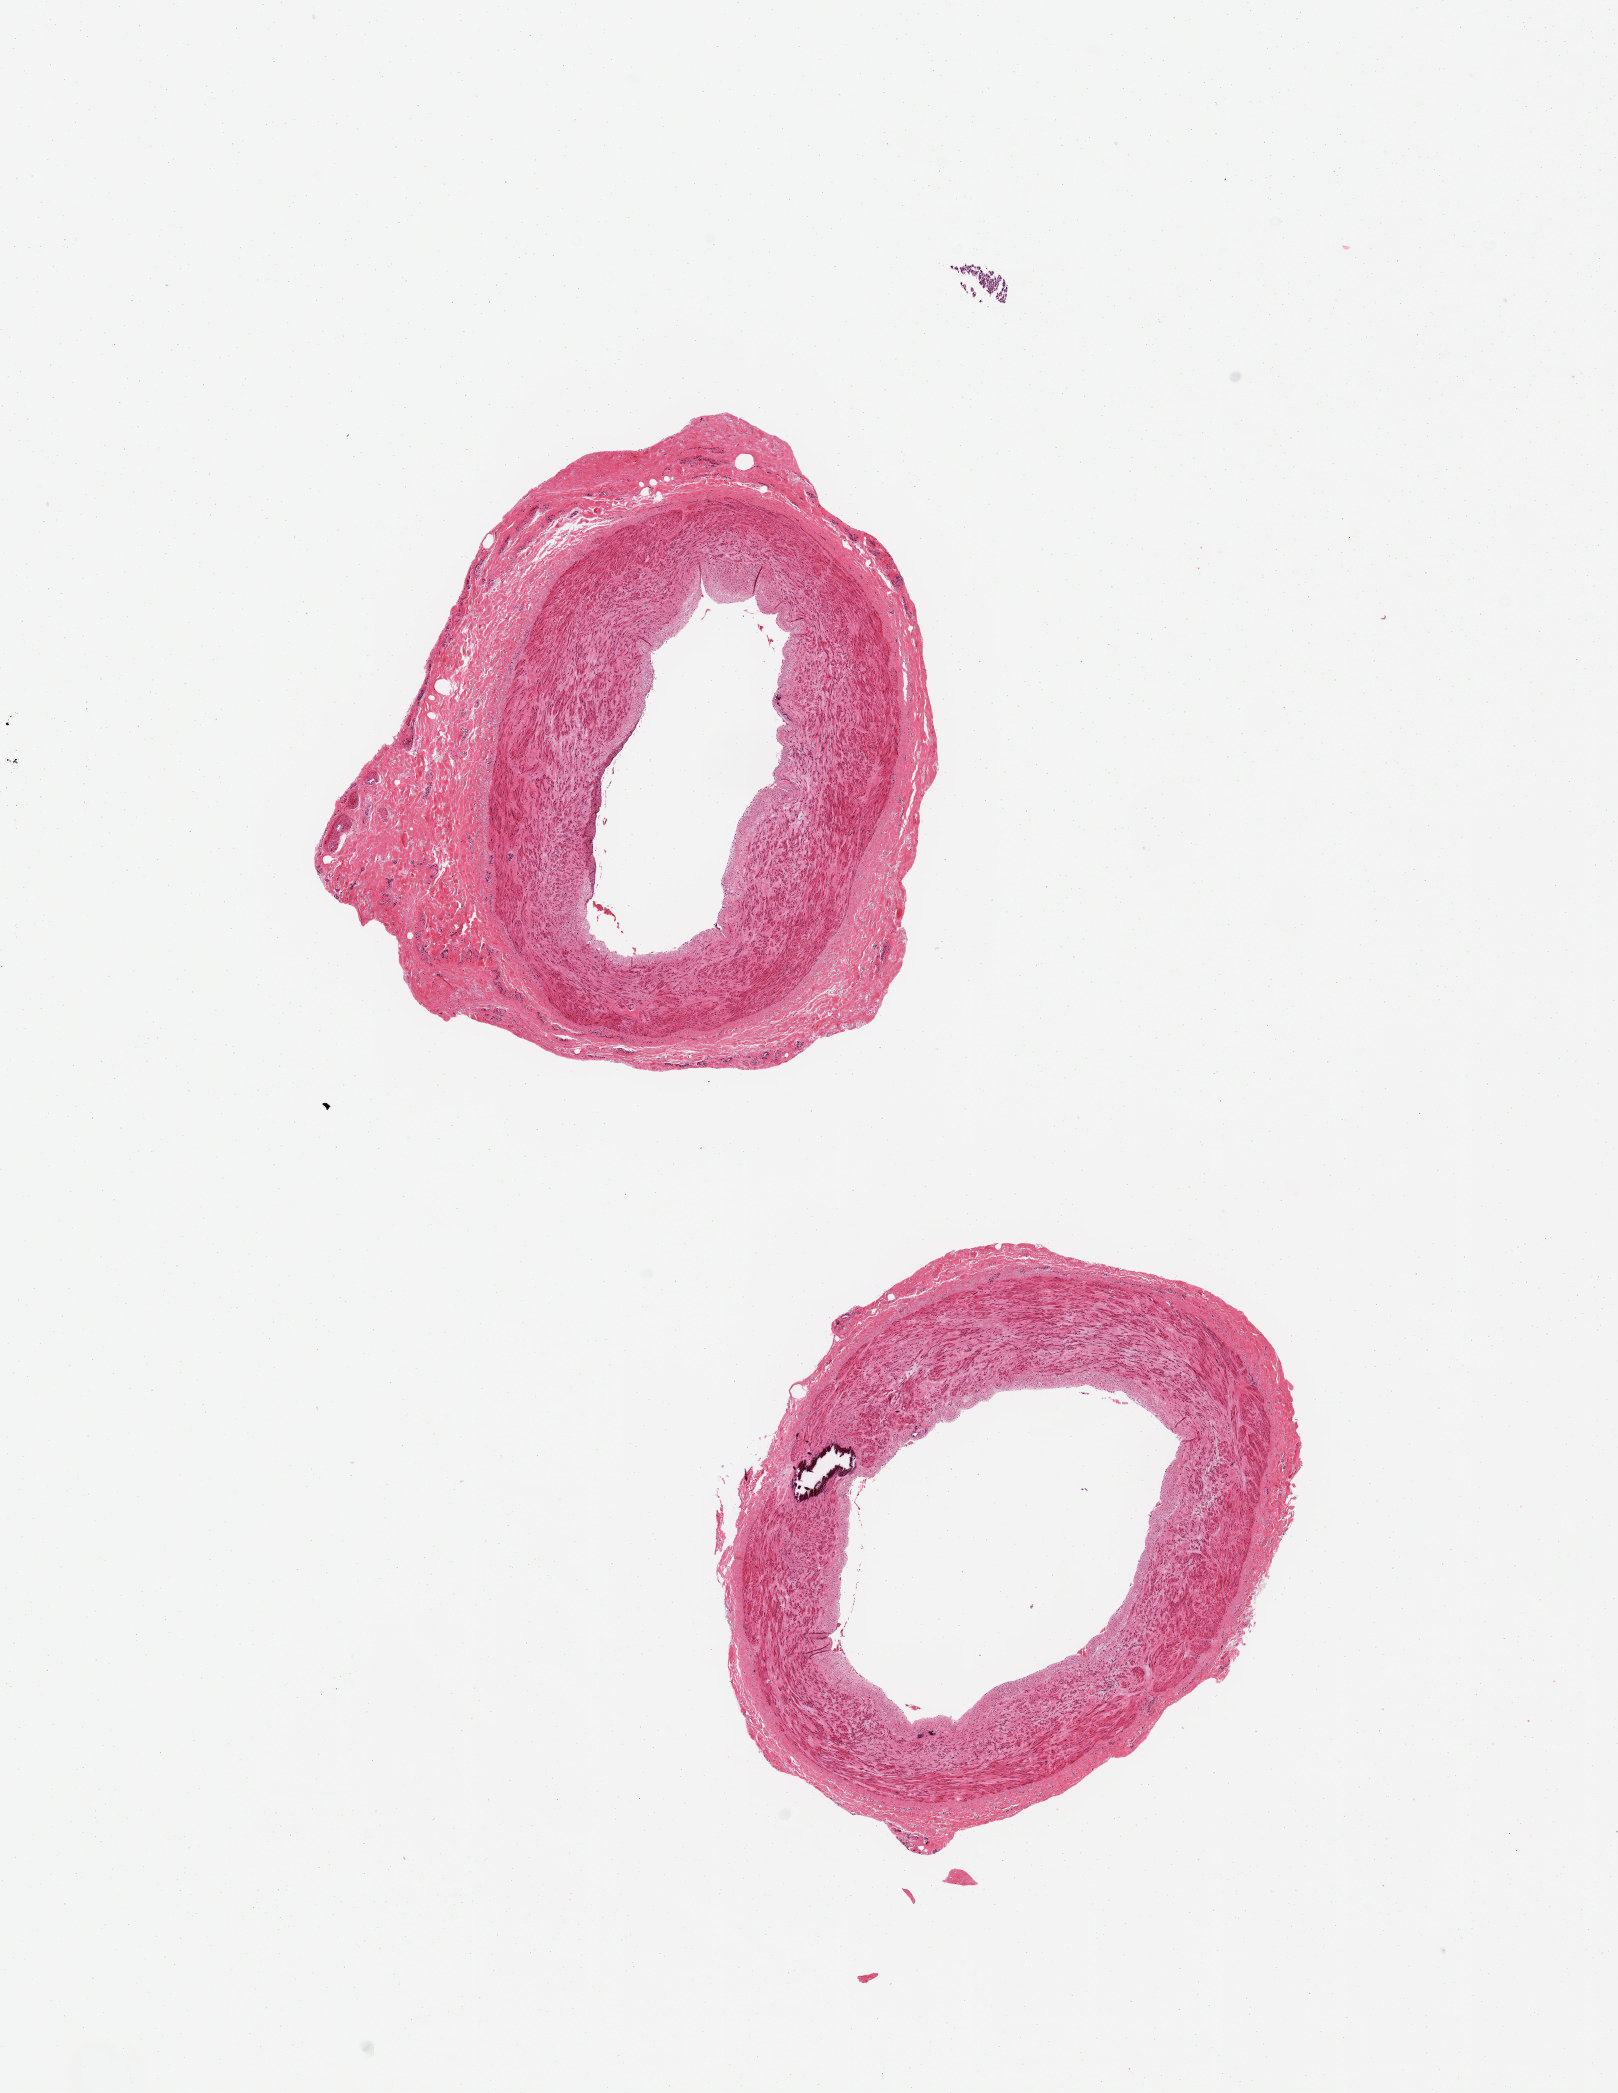
Digitized haematoxylin and eosin-stained section — shown as a low-resolution overview of the whole scanned area (about 12.8 x 16.6 mm); PAXgene-fixed, paraffin-embedded tissue; sampled site (target tissue): tibial artery; donor tissue sample. Male donor.
- reviewer comment on this tissue sample: 2 pieces; early atherosis; focal medial calcification; ~1.4mm attached adventitia